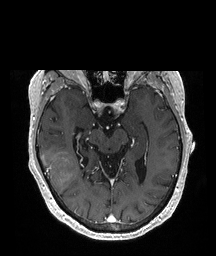
Brain MRI from a brain-tumour surgery series, one axial slice. Slice 125 of 208 in the series (ordered by position). T1-weighted post-contrast. 216 × 256 image matrix, field of view 216 × 256 mm. From the clinical record (not read from this slice): histopathology: Glioblastoma; WHO grade: 4; IDH mutation: no; tumour location: Right Temporal.
Annotated regions visible in this slice (expert manual segmentation):
- tumour: bounding box [x1, y1, x2, y2] px = [40, 152, 78, 194]